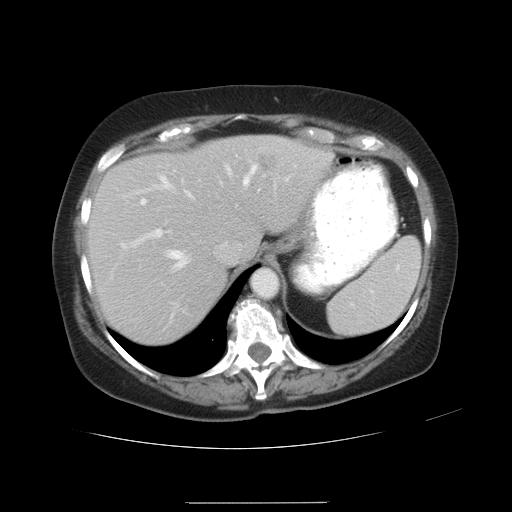
Contrast-enhanced abdominal CT, one axial slice. Slice 23 of 32 in the series (ordered by position). Reconstruction kernel STANDARD. 120 kVp. Intravenous contrast given. Soft-tissue window (W 400 / L 40 HU). 512 × 512 image matrix. Female patient, age 65 years. From the clinical record (not read from this slice): diagnosis: colorectal cancer liver metastases, imaged before liver resection; multiple liver metastases: yes.
Structures marked on this image (manually delineated by an expert):
- hepatic veins: bounding box <117,164,258,308> (left, top, right, bottom; pixels)
- liver: <91,138,326,345>
- planned liver remnant (the part of the liver to remain after resection): <91,145,238,344>
- portal vein (with intrahepatic branches): <120,201,171,250>
- liver metastasis: <260,157,277,173>